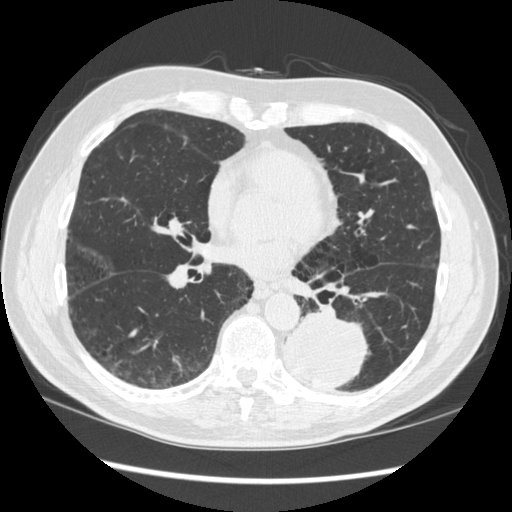
Low-dose screening chest CT, one axial slice; slice 149 of 348 in the series (ordered by position); reconstruction kernel STANDARD; lung window (W 1500 / L -600 HU); 1.25 mm slice thickness; 512 × 512 image matrix, field of view 360 × 360 mm.
Annotated regions visible in this slice (outlined manually by an expert reader):
- lesion 1 (tumor, lower lobe of left lung): bounding box [x1, y1, x2, y2] px = [284, 312, 369, 390]